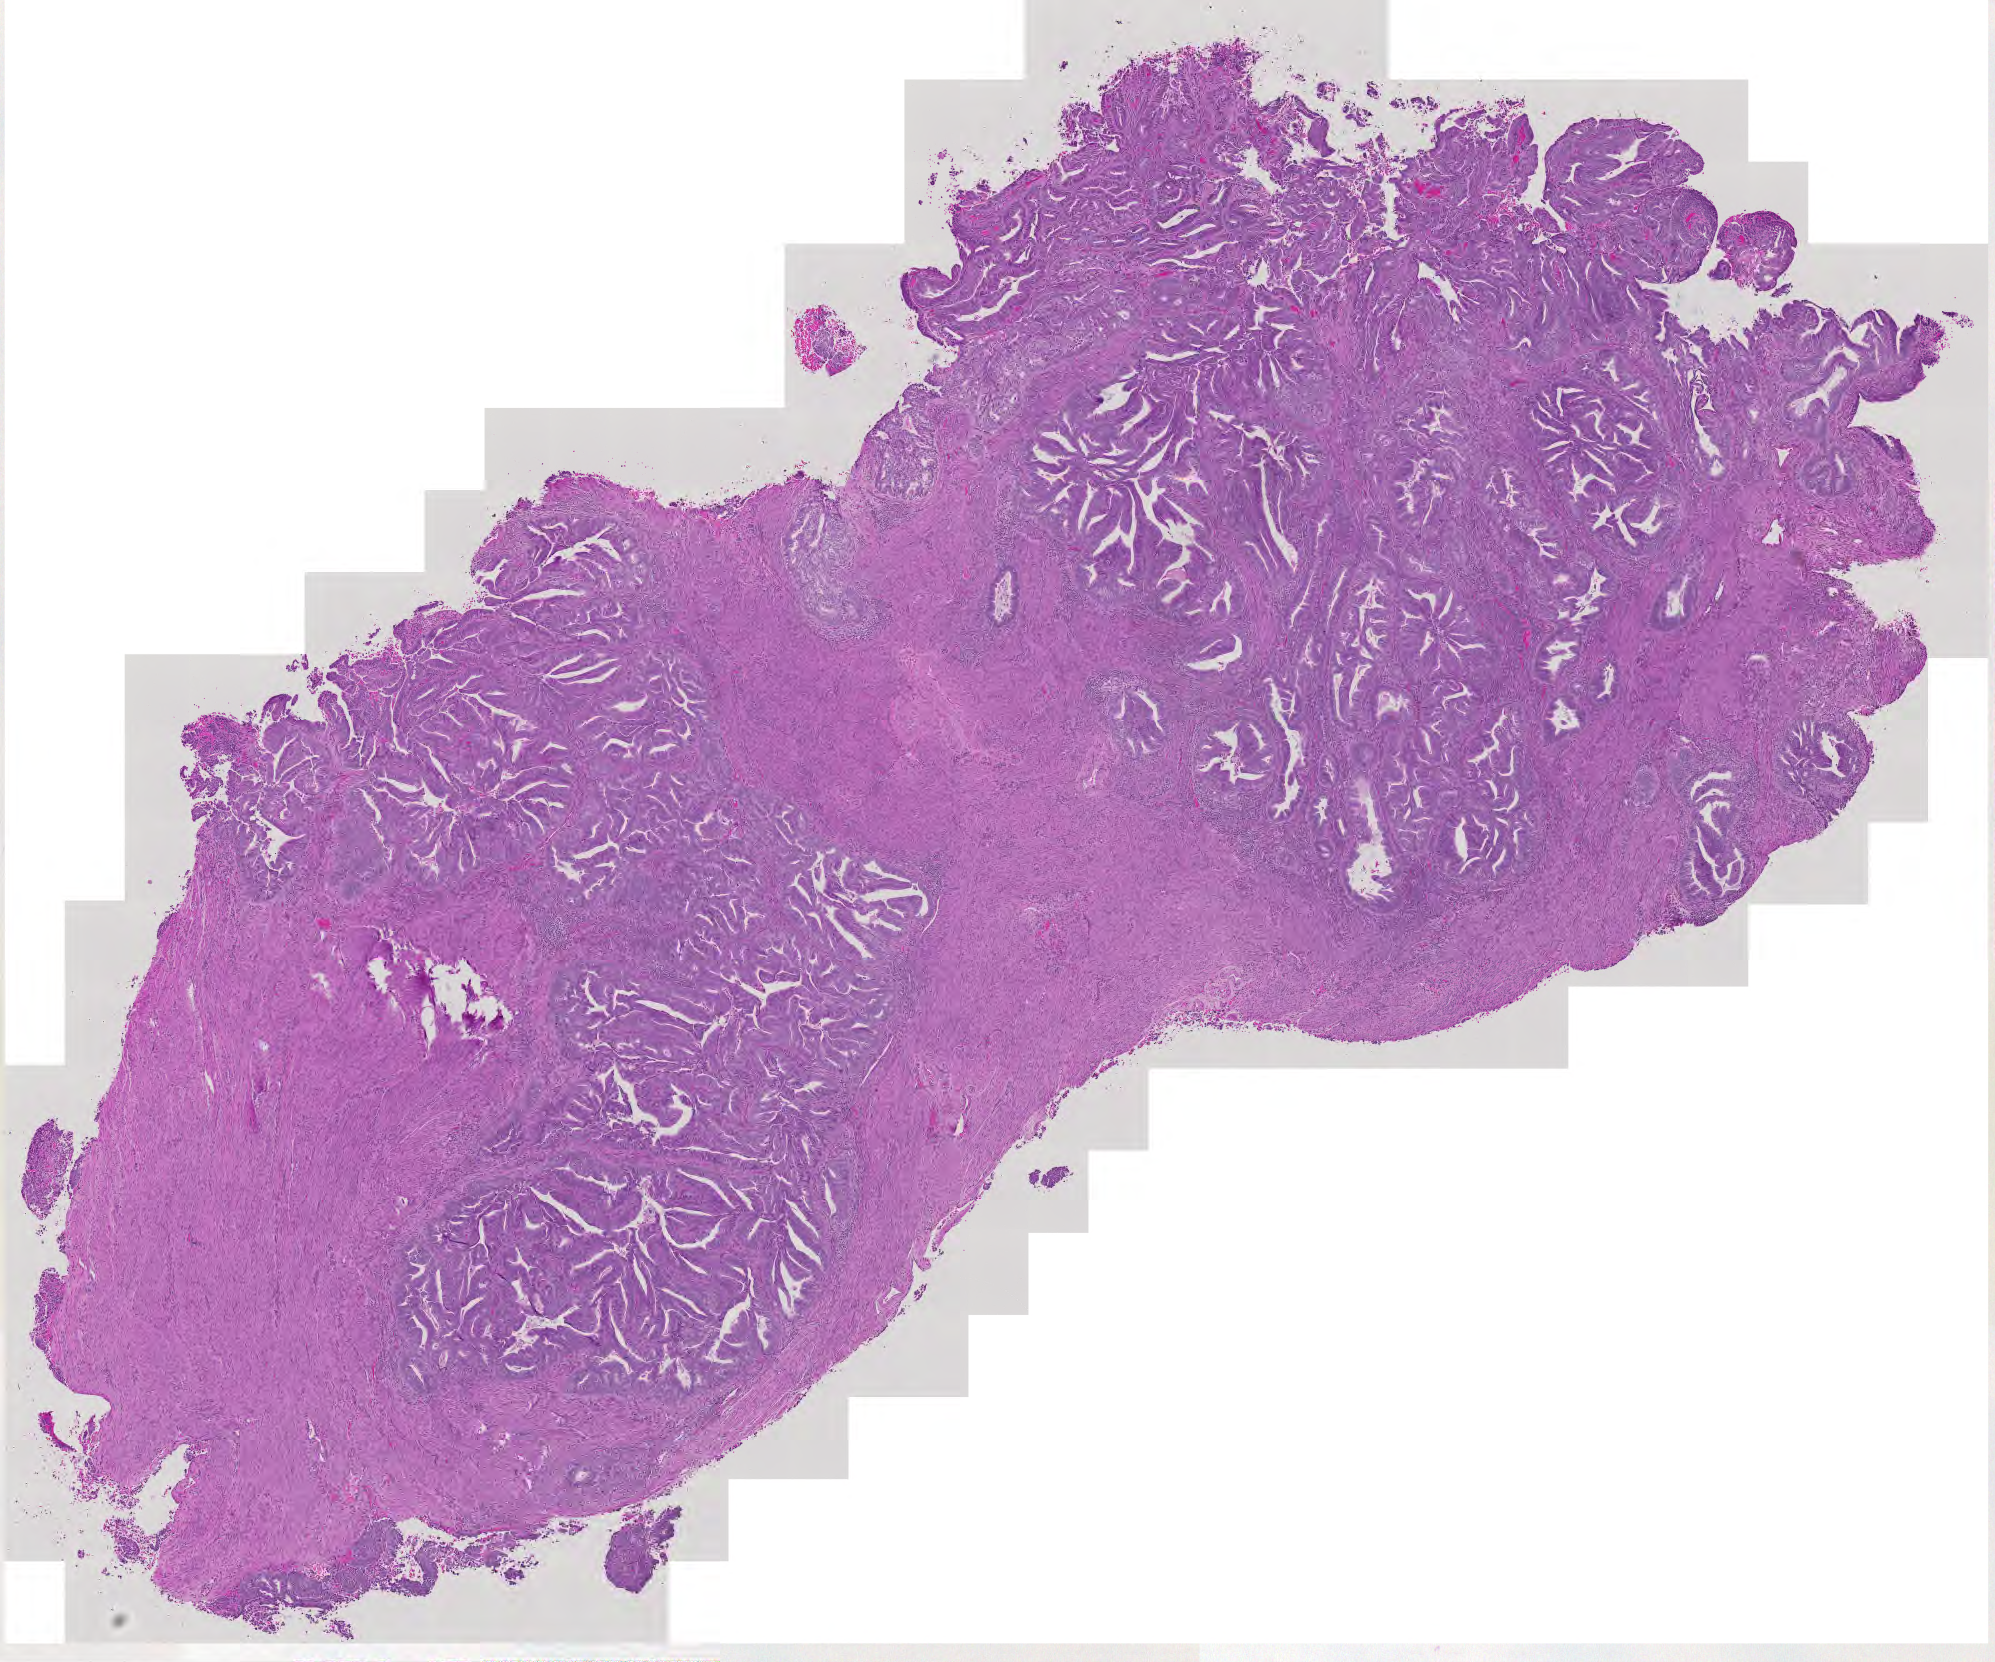
Digitized Hematoxylin and eosin (H&E) stained tissue section (whole slide), low-resolution overview of the scanned area, about 10.3 x 8.6 mm; tumour tissue sample, uterus. 54-year-old female patient.
Histologic diagnosis: Endometrioid adenocarcinoma, NOS.